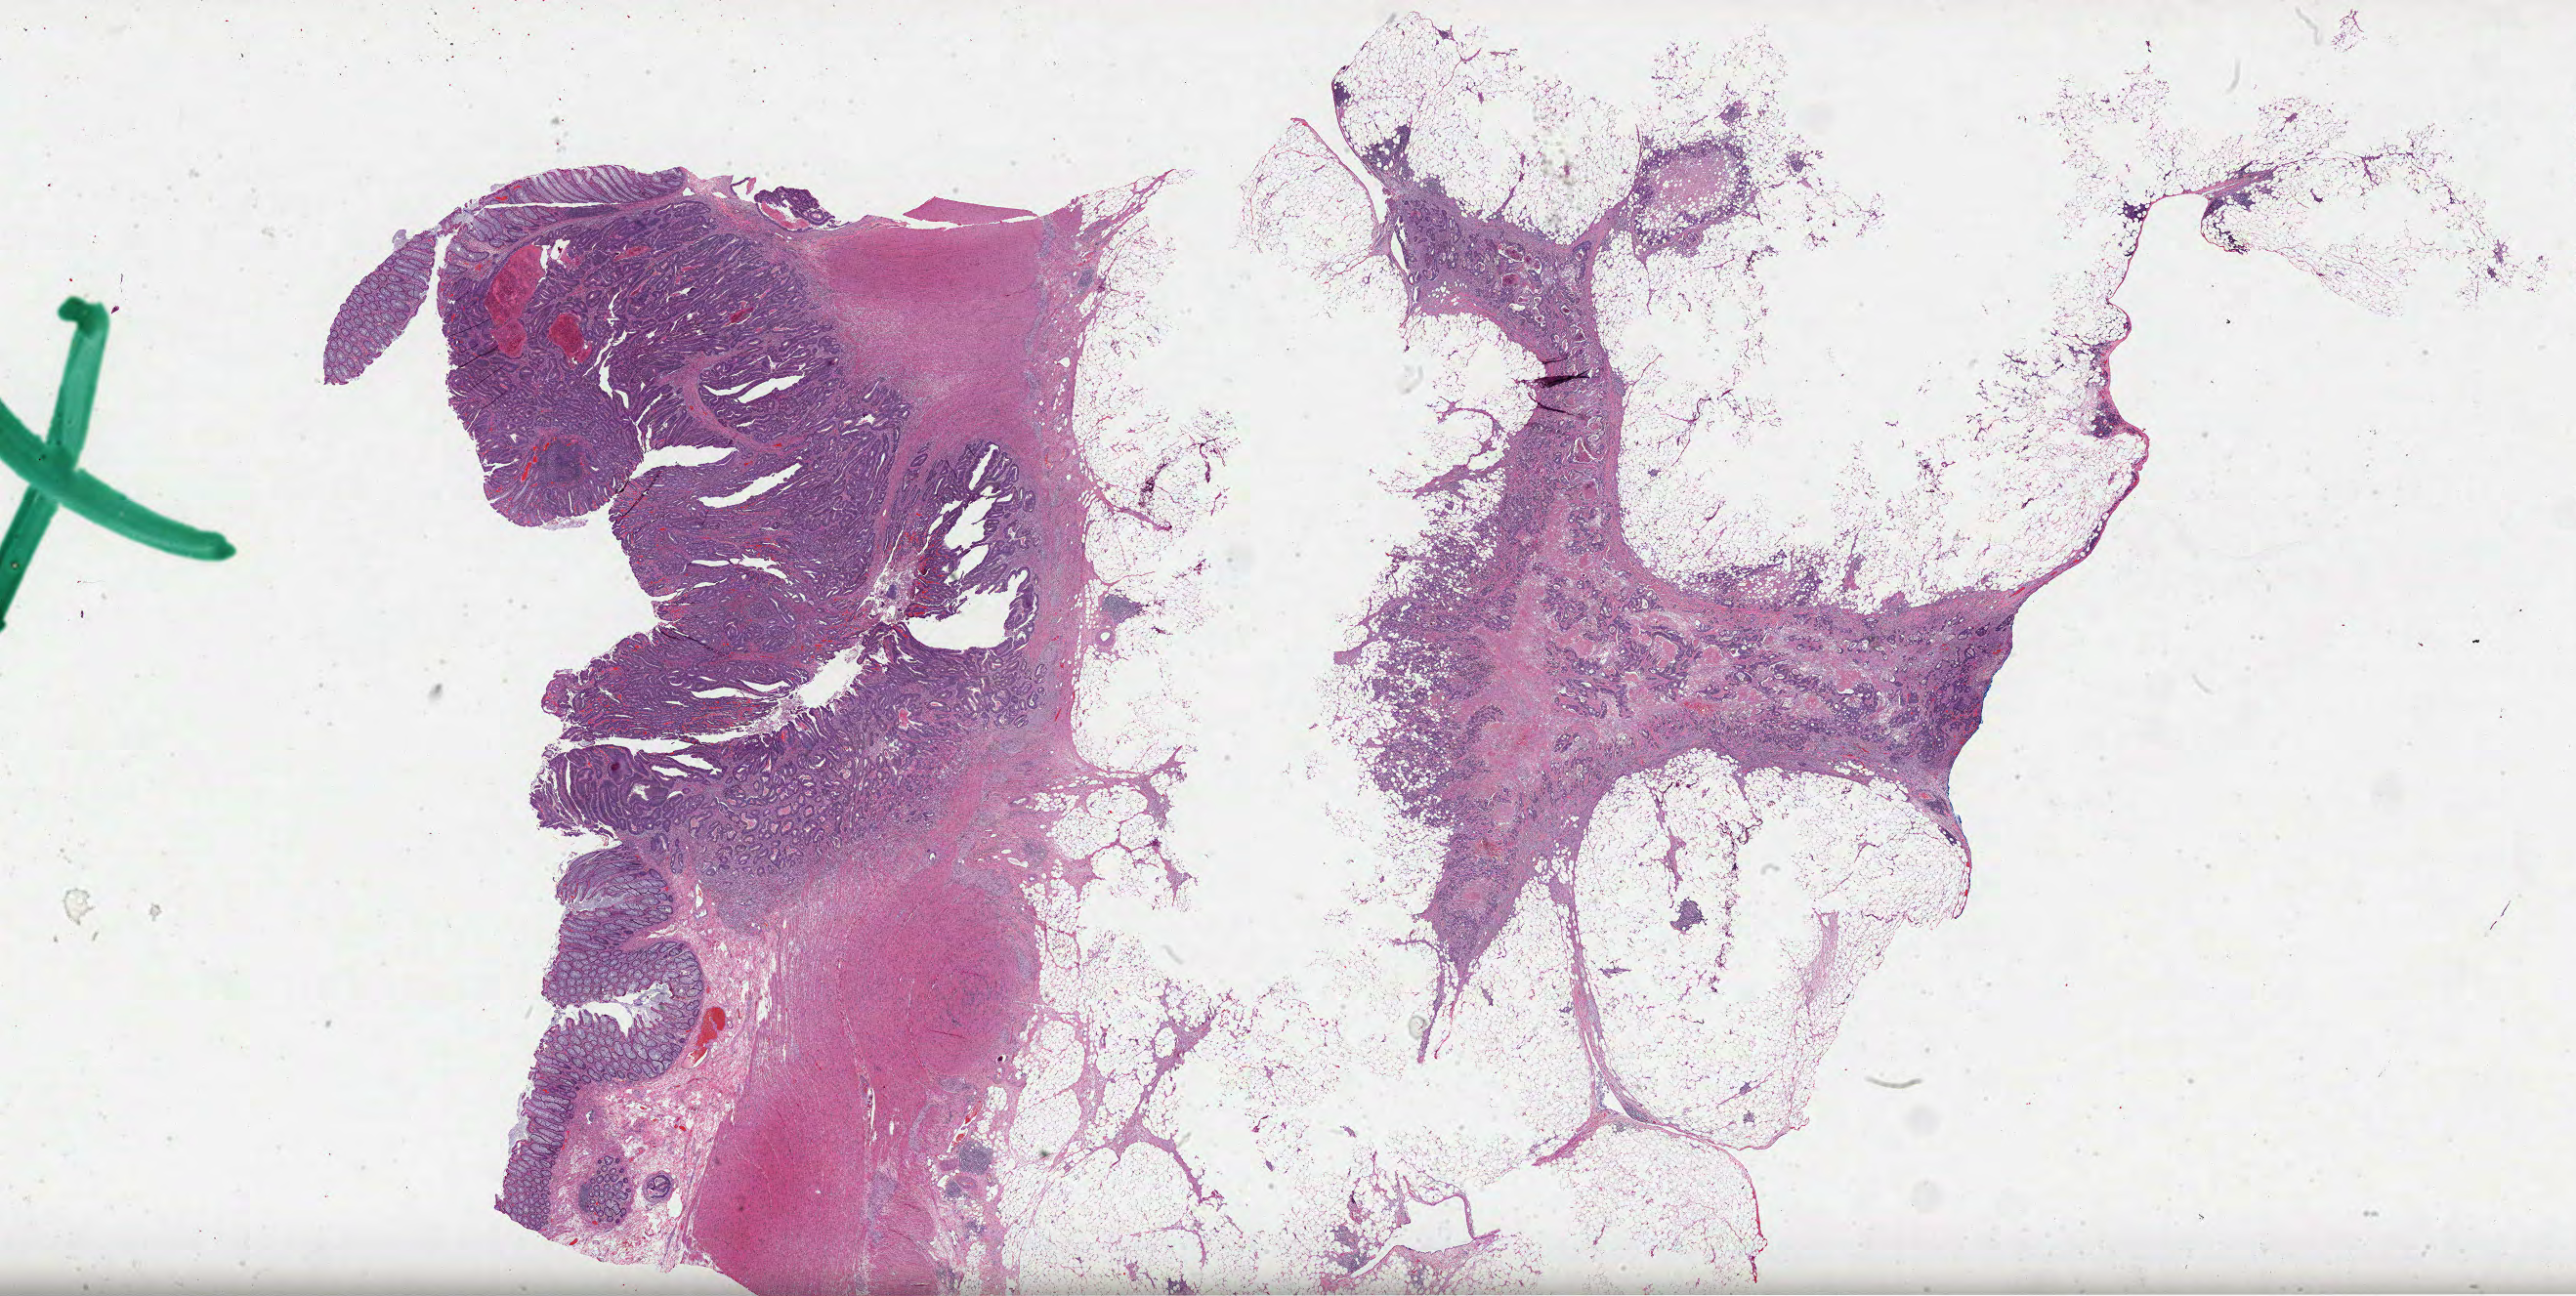
H&E-stained whole-slide image — shown as a low-resolution overview of the whole scanned area (about 42.5 x 21.4 mm). Formalin-fixed paraffin-embedded (FFPE) diagnostic section. Colon, primary tumour sample. Patient: female, age at initial diagnosis 59 years.
Diagnosis: Adenocarcinoma, NOS.